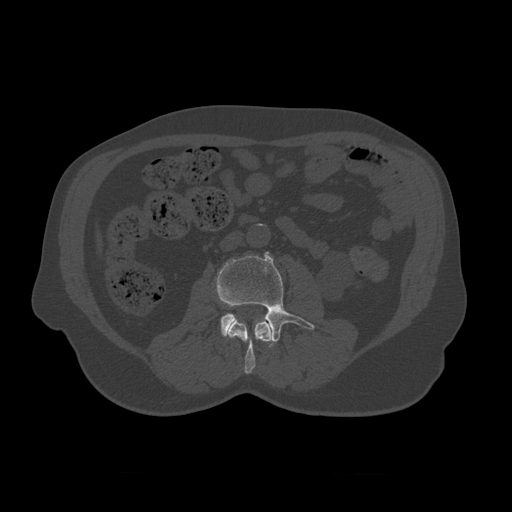
CT including the spine, one axial slice; slice 314 of 450 in the series (ordered by position); reconstruction kernel STANDARD; 120 kVp; bone window (W 1800 / L 400 HU); 1.25 mm slice thickness; 512 × 512 image matrix, field of view 405 × 405 mm. Patient age 75 years. Case-level facts recorded for this patient, not image findings: primary cancer: prostate.
Annotated regions visible in this slice (semi-automatic segmentation, software-assisted and operator-edited):
- L2 vertebra: box from (x=226, y=315) to (x=273, y=374) px
- L3 vertebra: (x=215, y=252)–(x=315, y=348)